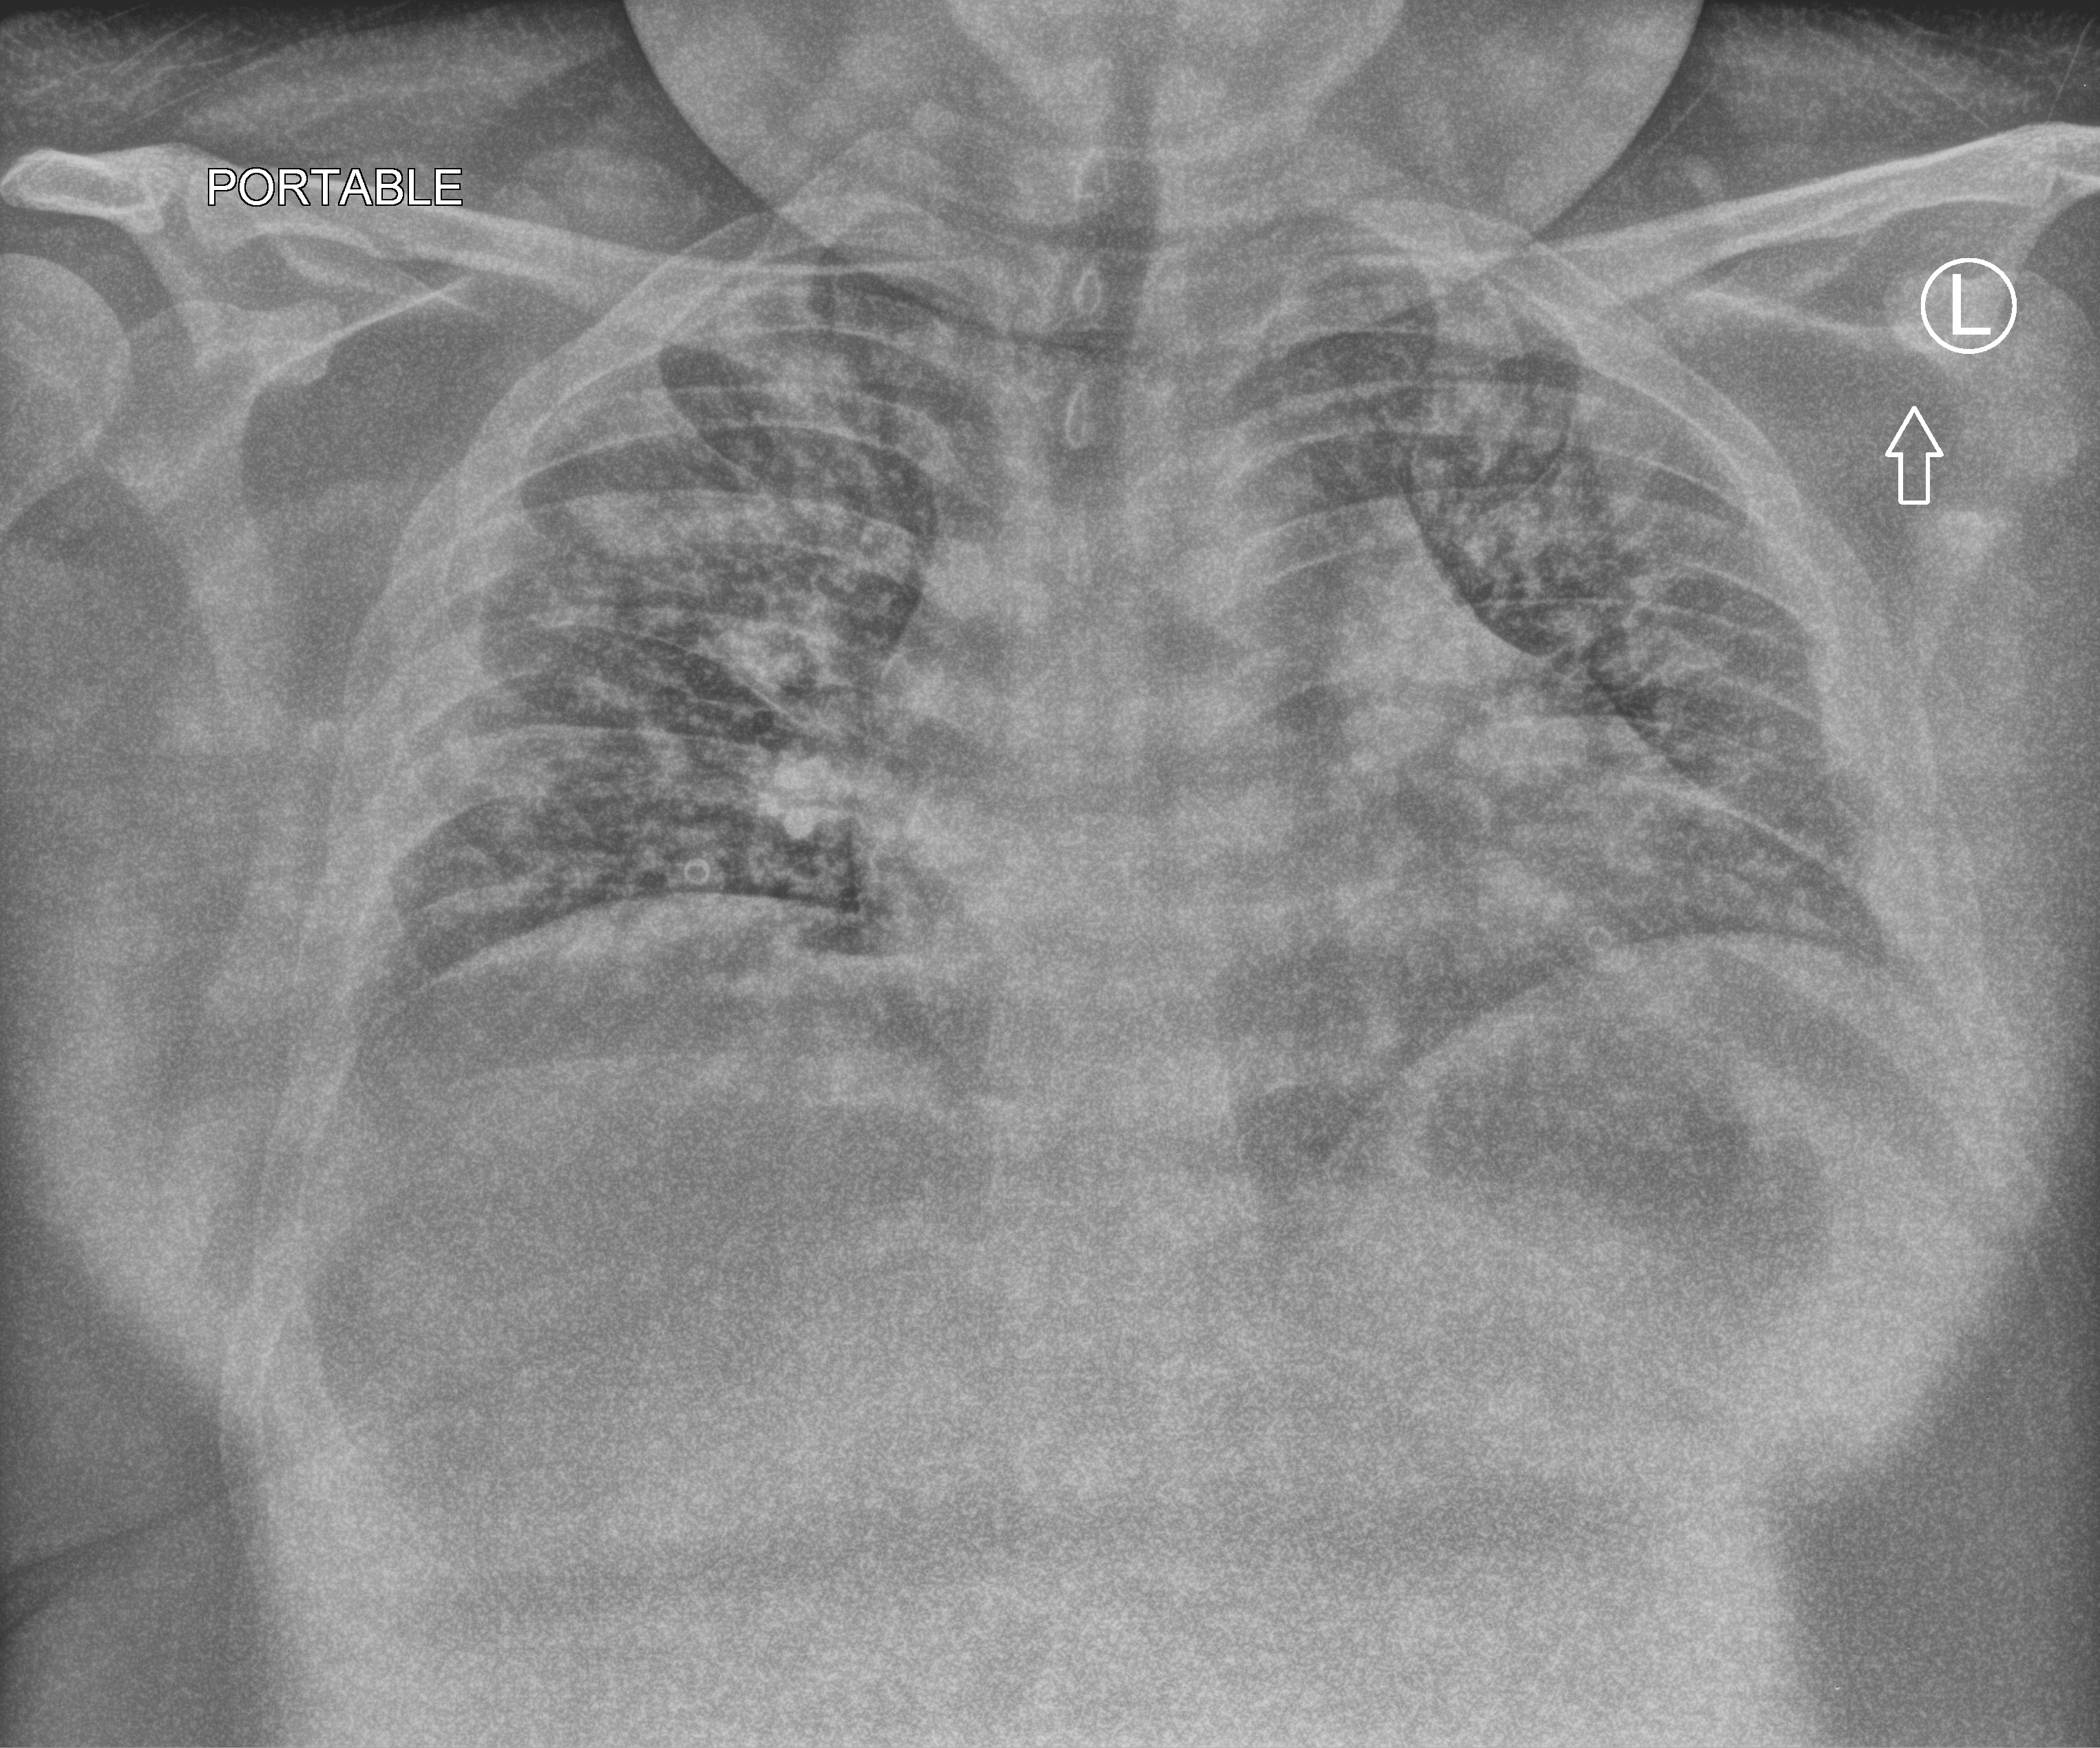
Bedside chest radiograph (computed radiography); anteroposterior (AP) projection. Patient hospitalised with COVID-19; male, aged 18–59 years.
Admission-level facts for this patient (not findings on this image; timing relative to this image not recorded): mechanically ventilated during this hospital stay: no.